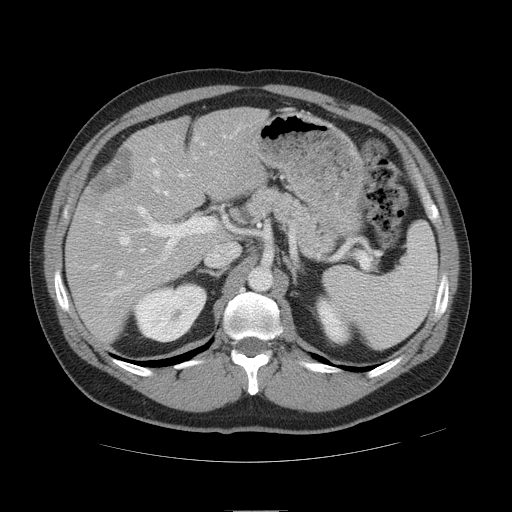
Contrast-enhanced abdominal CT, one axial slice; slice 29 of 49 in the series (ordered by position); reconstruction kernel STANDARD; 120 kVp; soft-tissue window (W 400 / L 40 HU); 5 mm slice thickness; 512 × 512 image matrix. Male patient, age 52 years. Case-level facts recorded for this patient, not image findings: diagnosis: colorectal cancer liver metastases, imaged before liver resection; multiple liver metastases: yes; largest metastasis: 5.1 cm; chemotherapy before resection: yes.
Outlined on this slice (manually delineated by an expert):
- hepatic veins: bounding box (x1, y1, x2, y2) in pixels: (117, 137, 206, 276)
- liver: (66, 108, 263, 339)
- planned liver remnant (the part of the liver to remain after resection): (132, 108, 263, 205)
- portal vein (with intrahepatic branches): (105, 136, 225, 303)
- liver metastasis: (92, 149, 135, 196)